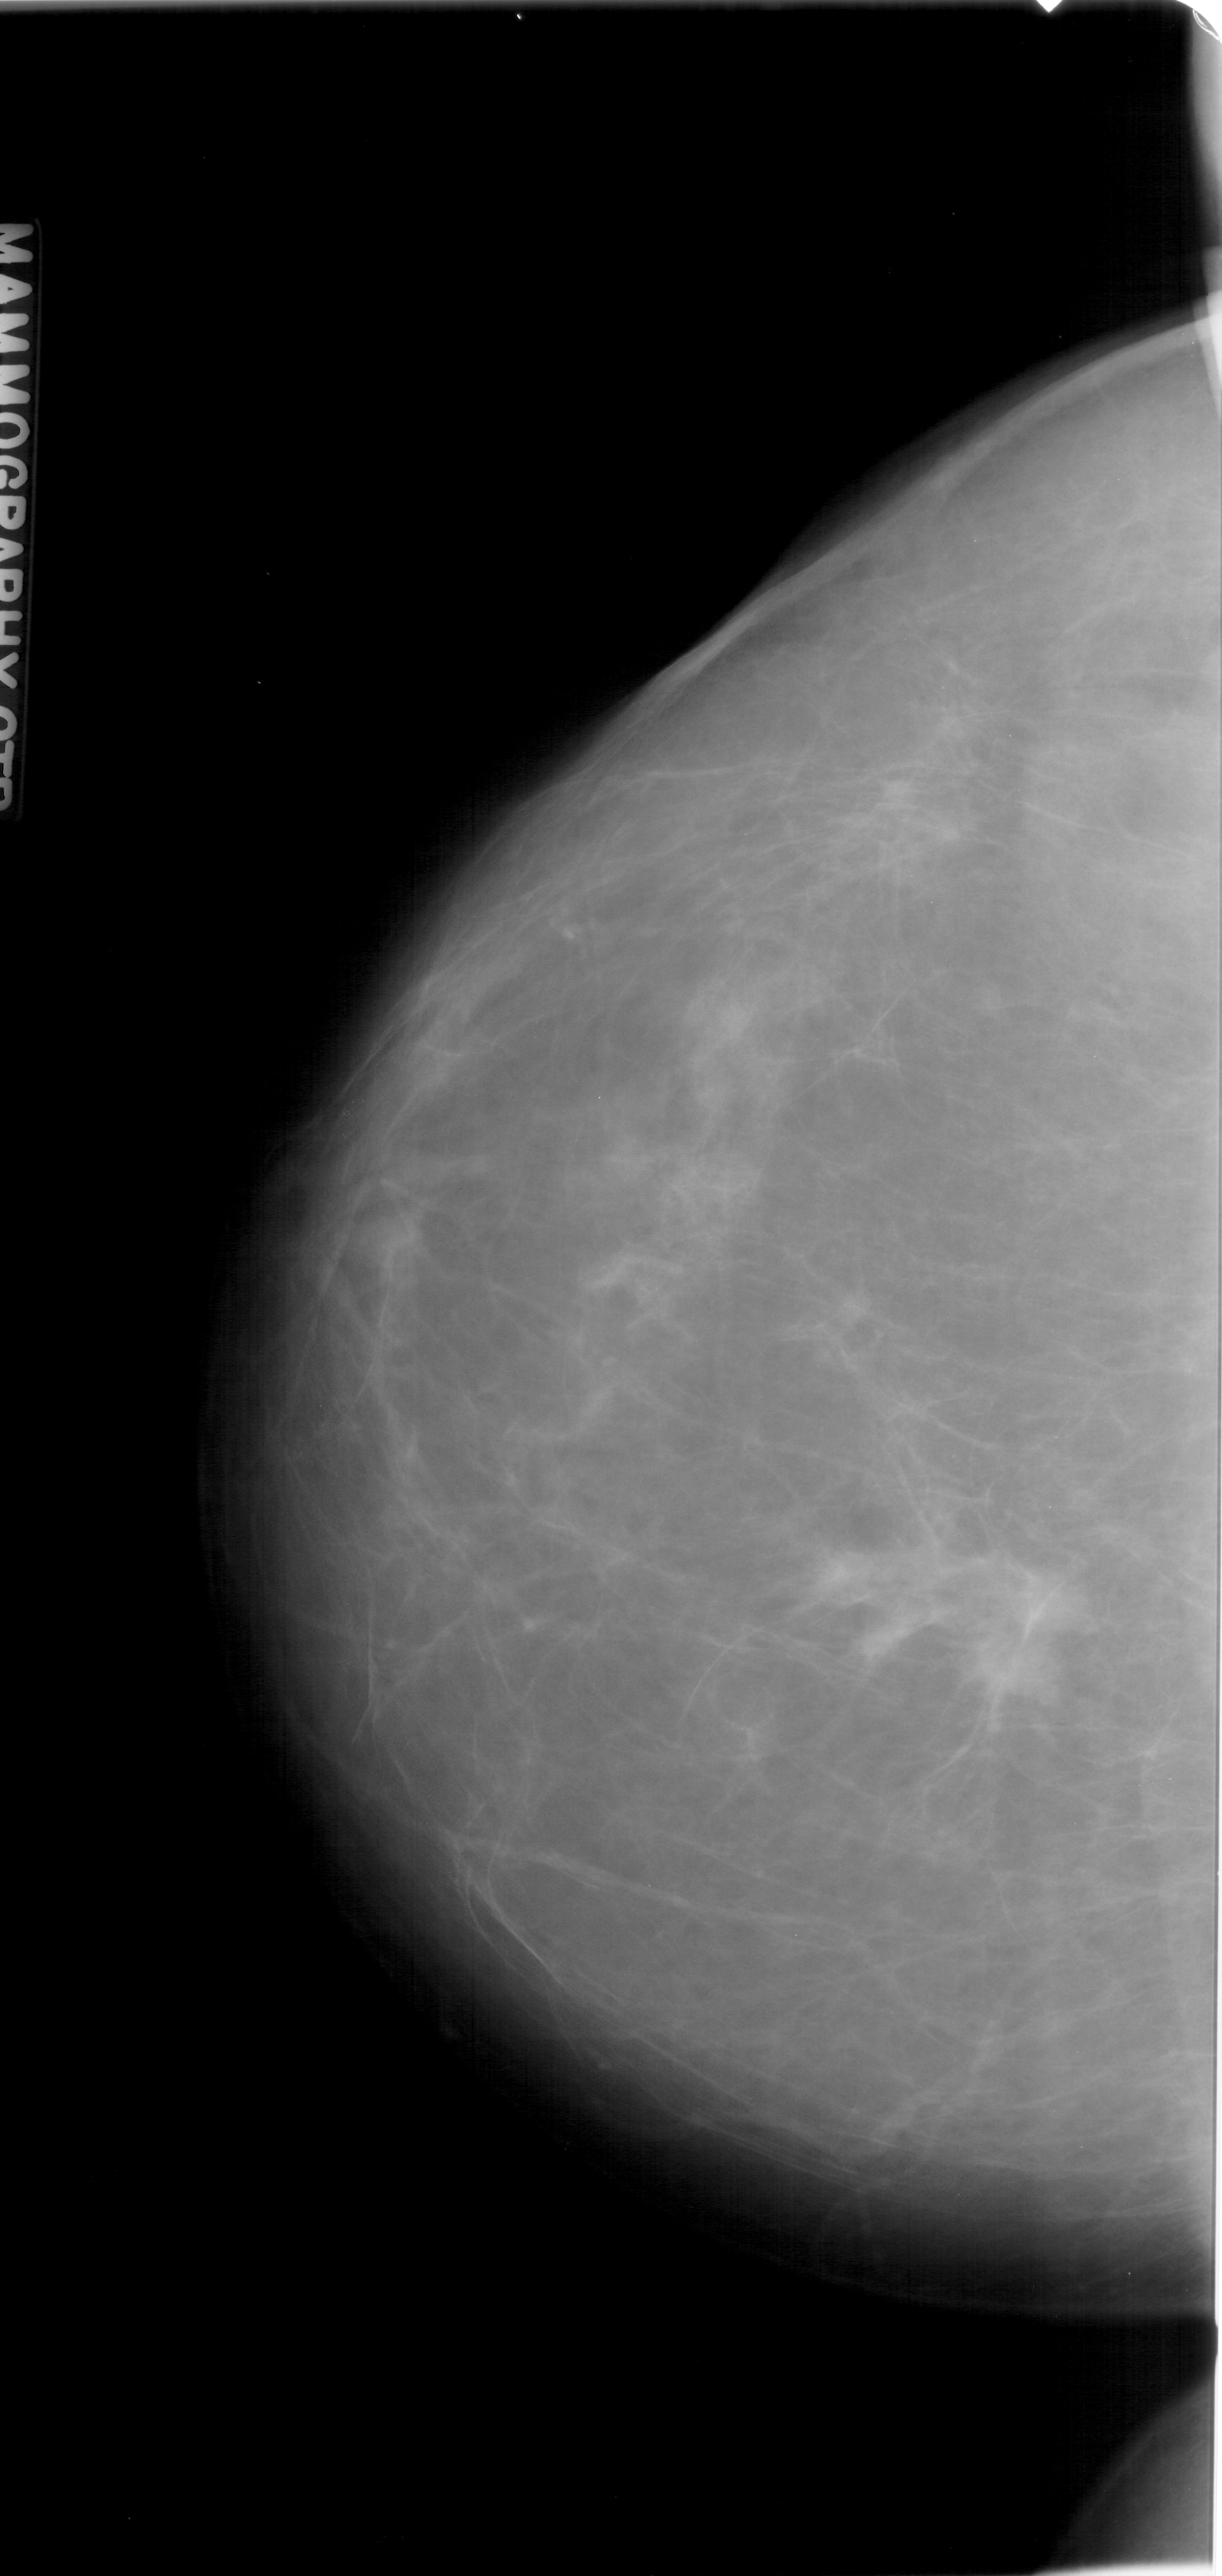
Scanned film-screen mammogram, left breast, craniocaudal (CC) view, breast composition: scattered fibroglandular densities (BI-RADS density category 2 of 4).
Marked findings (only marked abnormalities are described; nothing is implied about the rest of the image): mass, shape irregular, margins ill defined; BI-RADS assessment category 4; subtlety rating 5 on a 1 (subtle) to 5 (obvious) scale; pathology (as recorded): malignant.